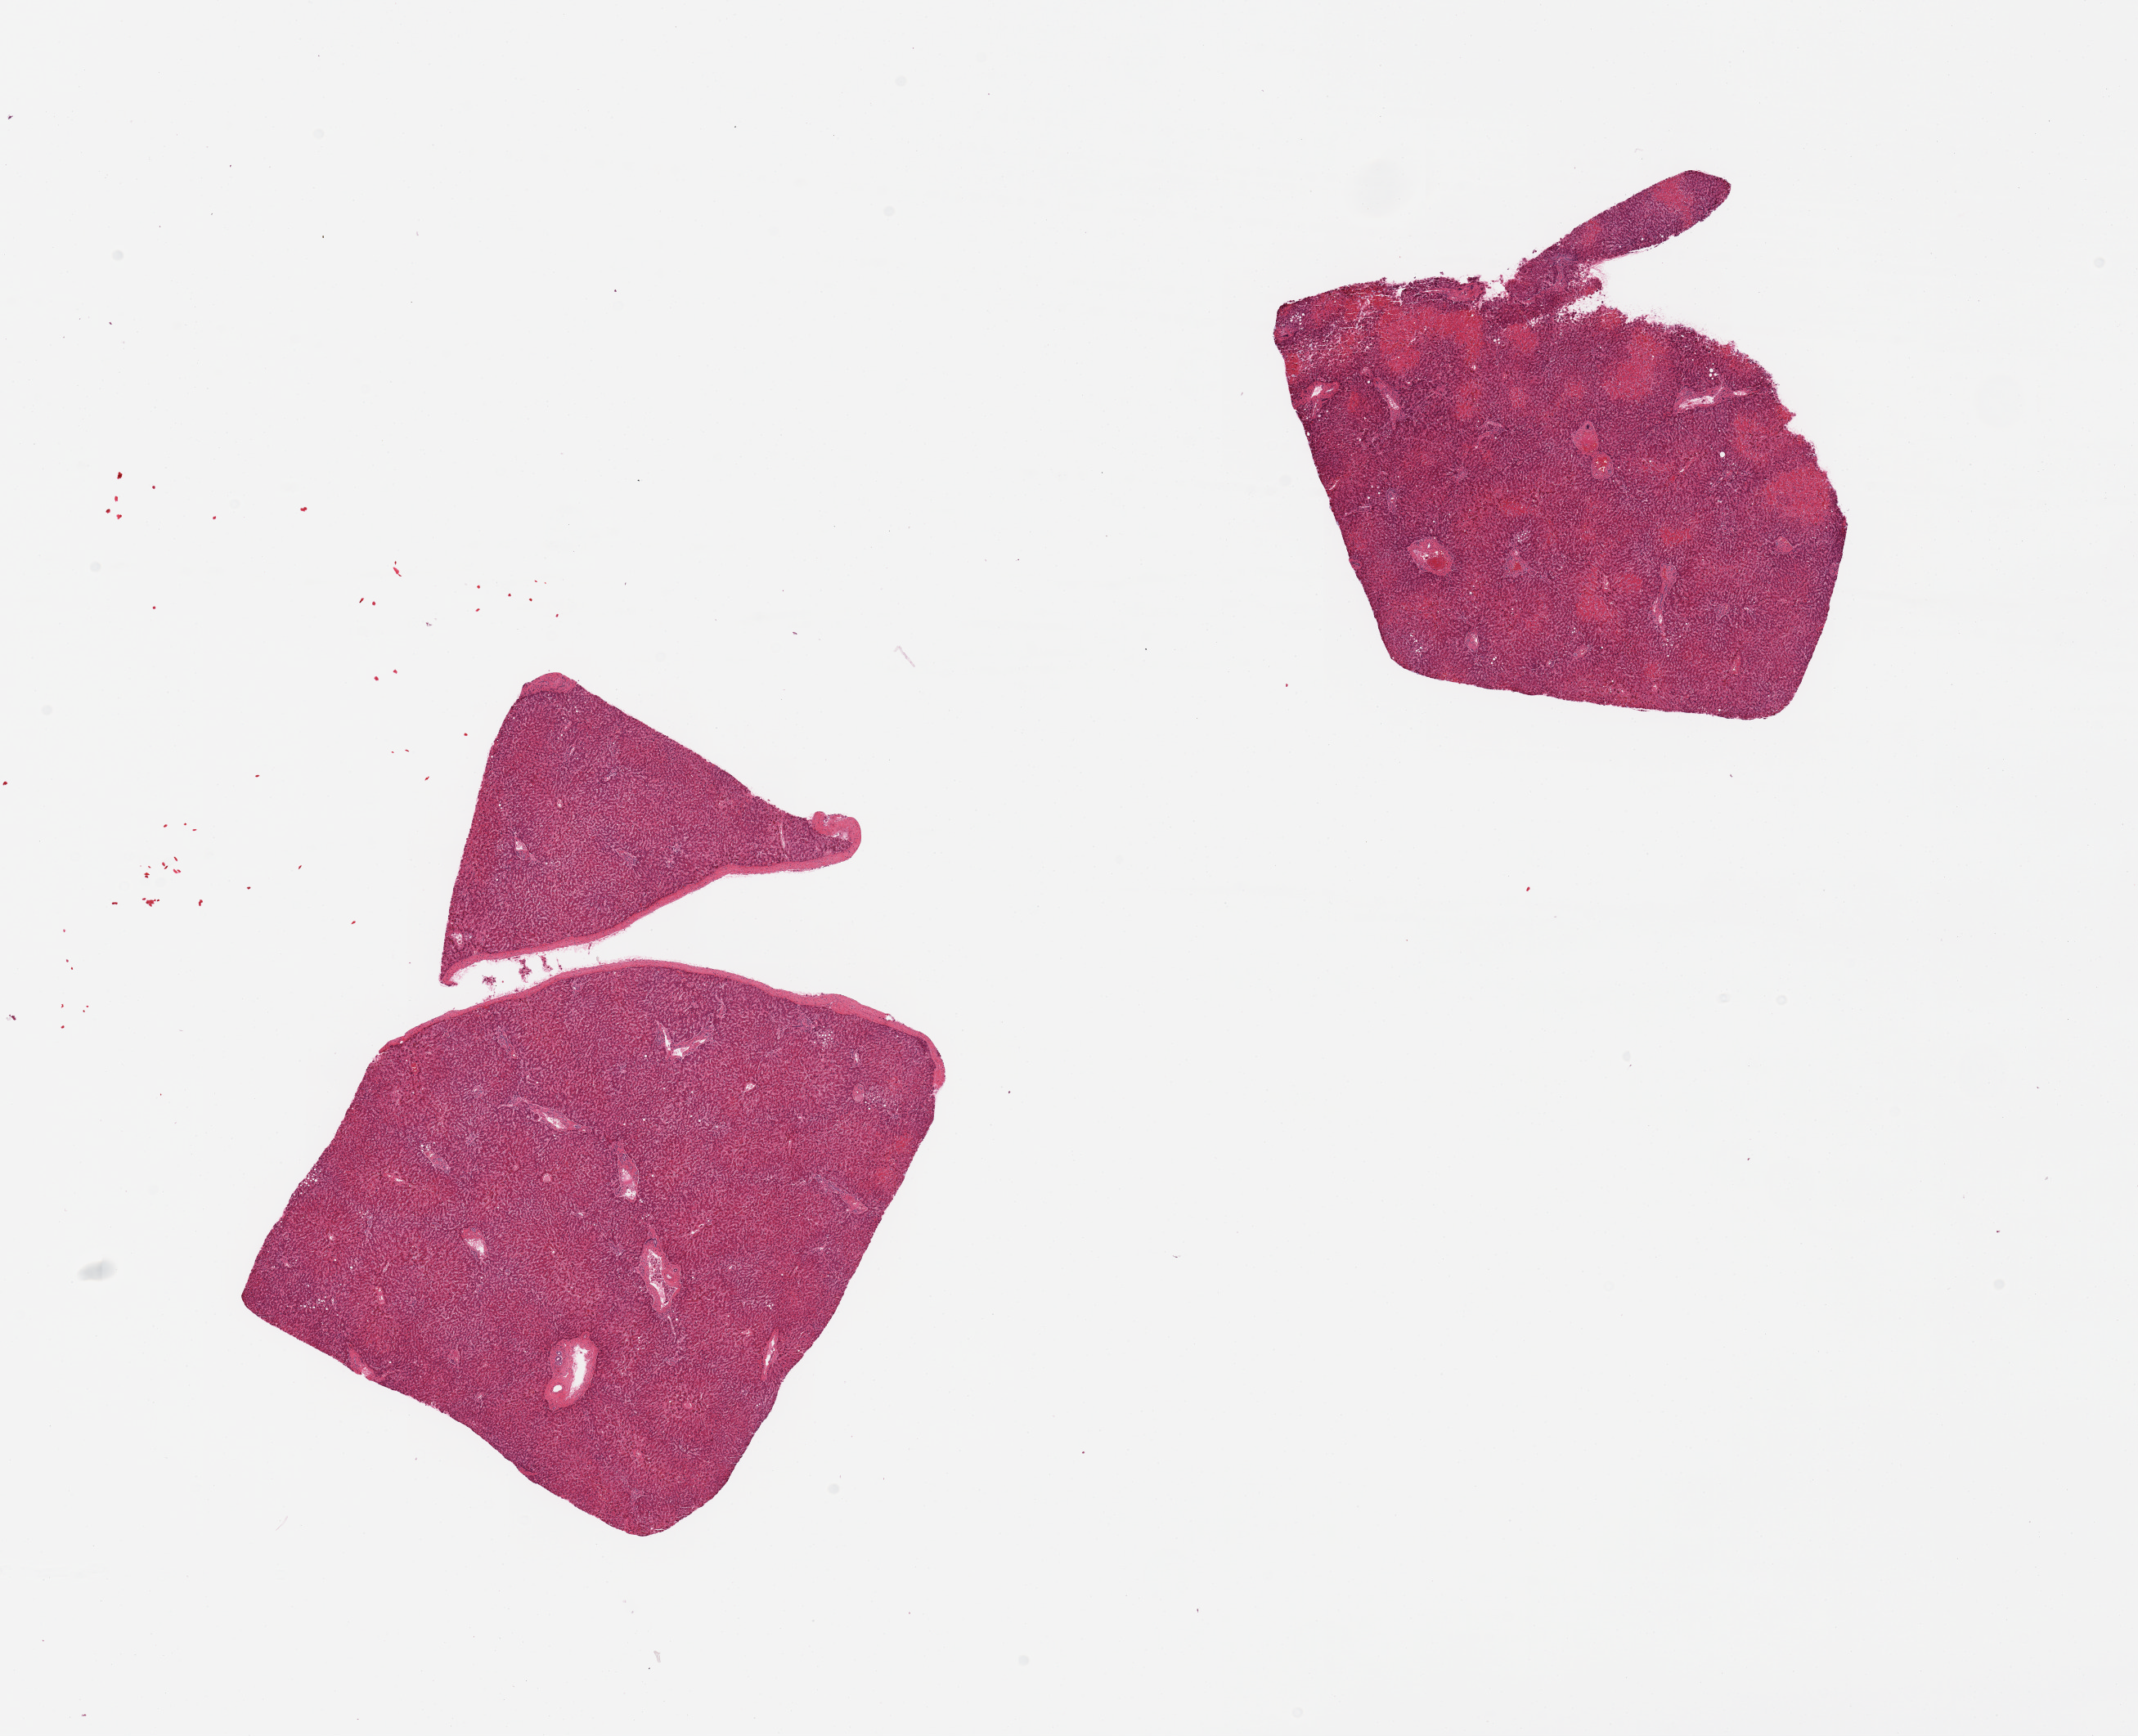
Digitized haematoxylin and eosin-stained section, low-resolution overview of the scanned area, about 20.7 x 16.8 mm (slide scanned at 20x). PAXgene-fixed paraffin-embedded (PFPE) section. Target tissue: liver. Donor tissue sample. Donor: male.
Reviewer comment on this tissue sample: 2 pieces, diffuse mild micro/macrovesicular steatosis, moderate congestion.